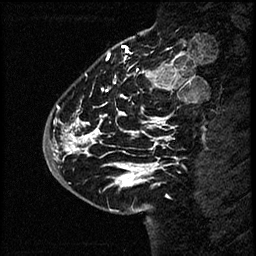
Breast MRI (dynamic contrast-enhanced), one sagittal slice; slice 19 of 60 in the series (ordered by position); dynamic contrast-enhanced study with each time point stored as its own series, time point 2 of 4 at this slice position (early post-contrast, ordered by acquisition time); 1.5 T; TE 4.2 ms, TR 17.6 ms; 256 × 256 image matrix, field of view 200 × 200 mm. Patient: female, 43 years. Case-level facts recorded for this patient, not image findings: setting: breast cancer imaged before/during neoadjuvant chemotherapy.
Annotated regions visible in this slice (semi-automatic segmentation, software-assisted and operator-edited):
- analysis volume of interest (the breast-tissue region the enhancement analysis was run in; not a lesion): bounding box [x1, y1, x2, y2] px = [47, 56, 169, 191]
- tumour enhancement mask (voxels above the 100 % enhancement threshold inside the analysis volume of interest): [51, 71, 169, 185]